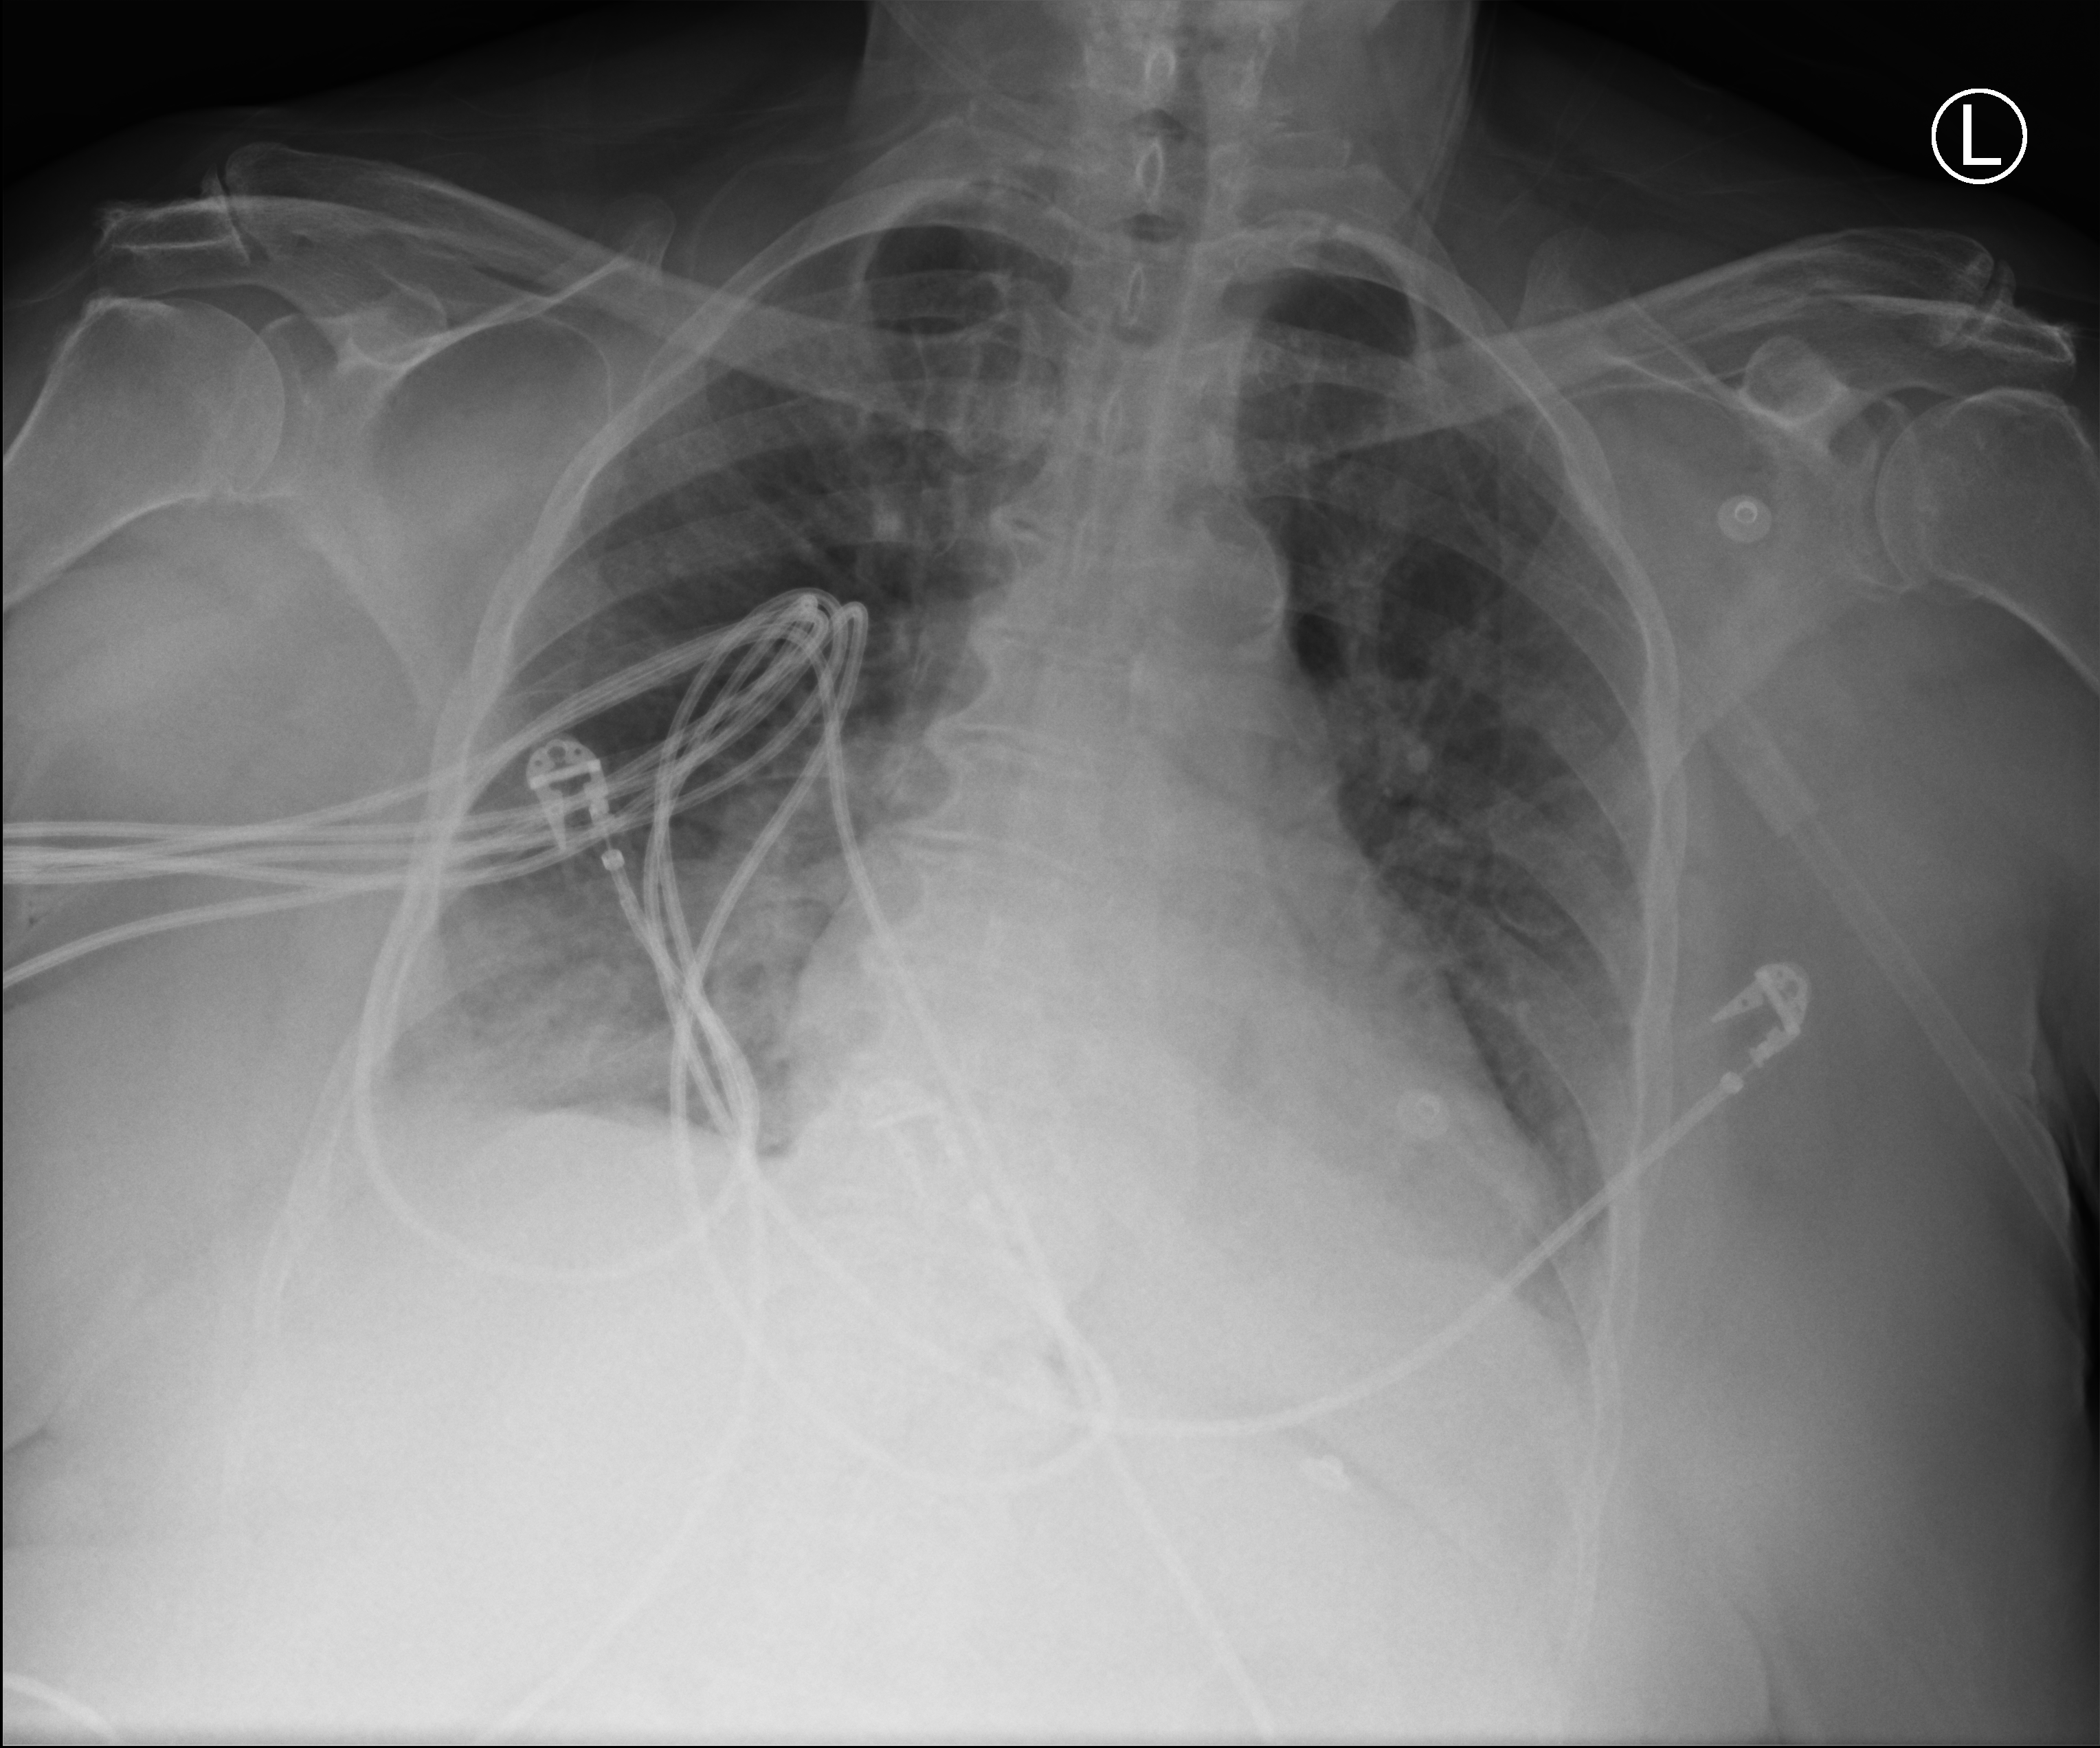
Bedside chest radiograph (computed radiography), anteroposterior (AP) projection. Female patient hospitalised with COVID-19, age 75–90 years.
From the hospital-stay record, not from the radiograph (when in the stay this image was taken is not recorded): admitted to intensive care during this hospital stay: no; length of hospital stay: 4 days.